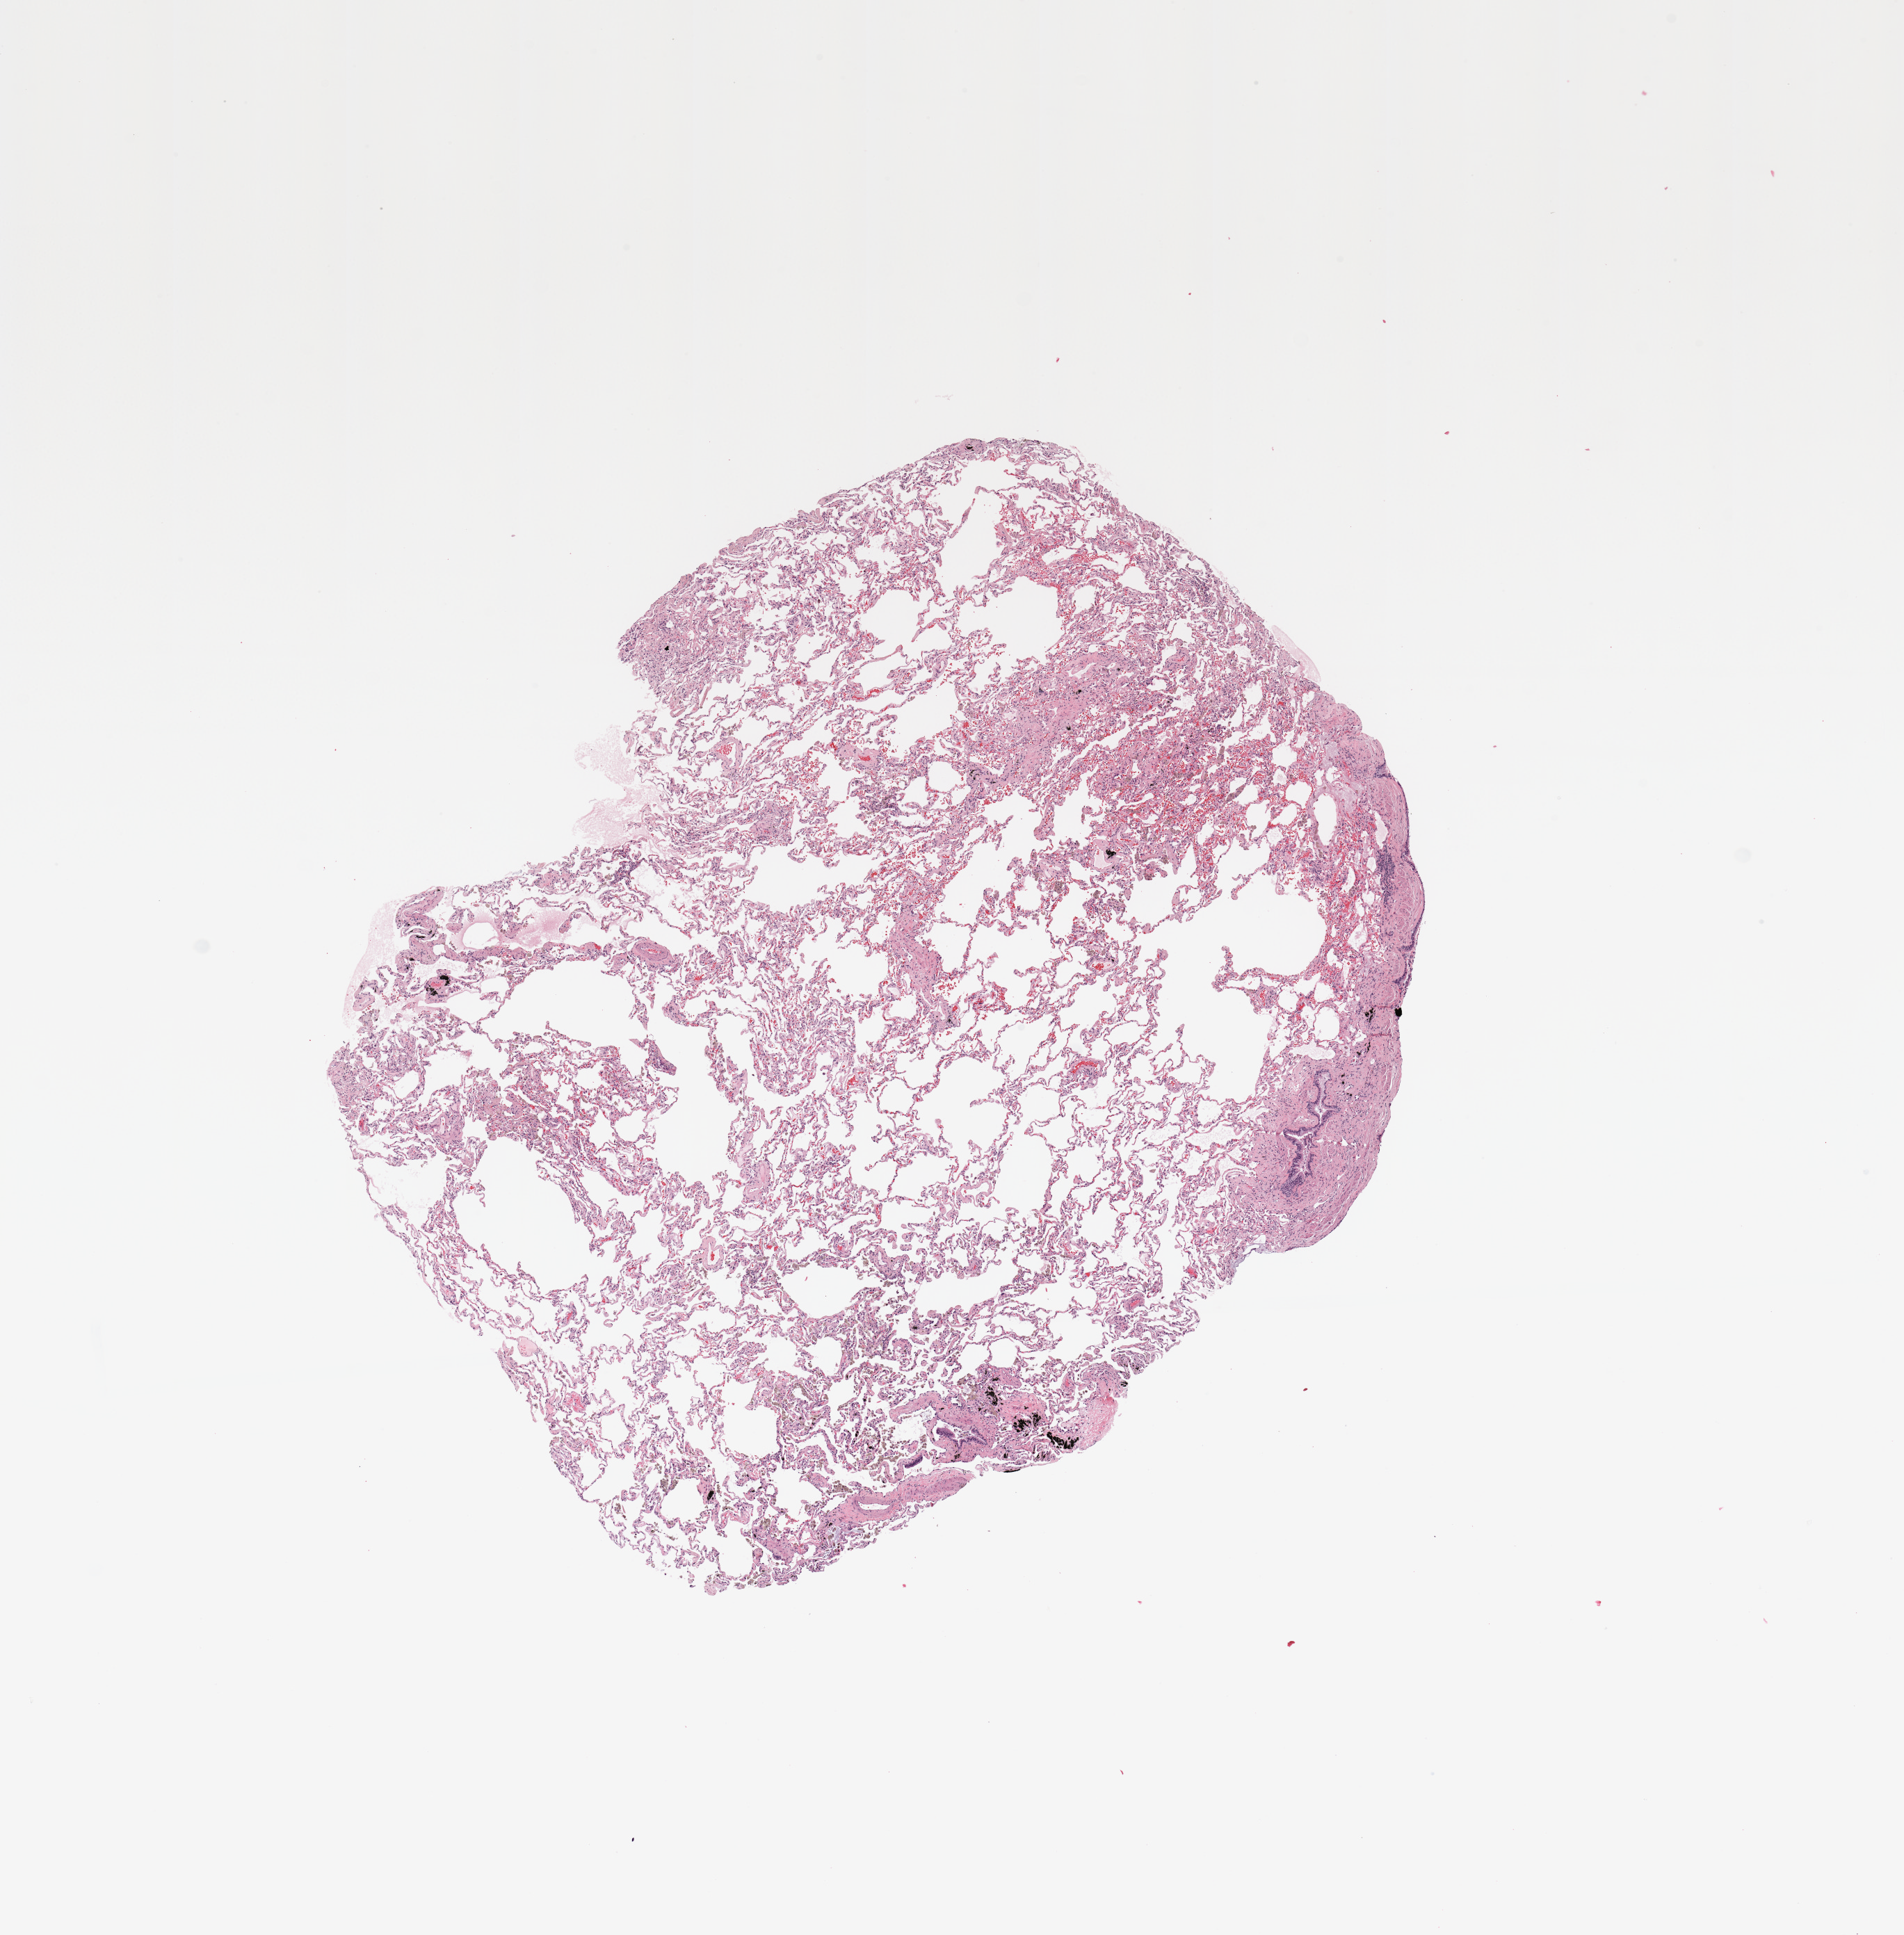
H&E-stained whole-slide image, low-resolution overview of the scanned area, about 10.8 x 11.0 mm (from a 20x scan), normal (non-tumour) tissue sample, sampled site: lung. 61-year-old male patient.
This section: normal (non-tumour) tissue from the same patient. Patient diagnosis: Adenocarcinoma, NOS.